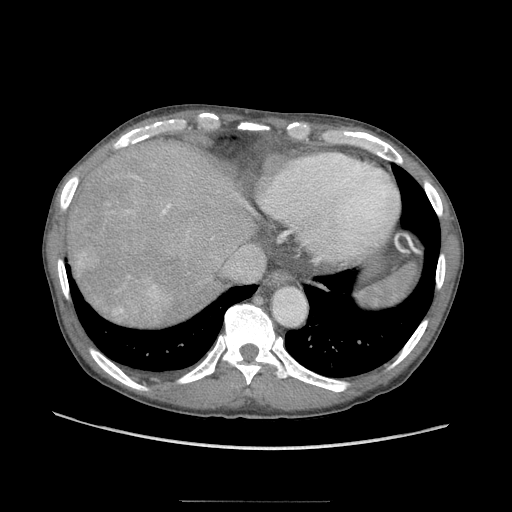
Contrast-enhanced abdominal CT (liver protocol), one axial slice. 120 kVp. Soft-tissue window (W 400 / L 40 HU). 2.5 mm slice thickness. 512 × 512 image matrix, field of view 380 × 380 mm. Case-level facts recorded for this patient, not image findings: diagnosis: hepatocellular carcinoma (patient treated with transarterial chemoembolisation; whether this scan precedes or follows treatment is not stated here); TNM stage (as recorded): Stage-IIIA; Child-Pugh class: A; tumour differentiation: moderately differentiated; tumour nodularity: multinodular.
Annotated regions visible in this slice (semi-automatic segmentation, software-assisted and operator-edited):
- abdominal aorta: box from (x=274, y=289) to (x=305, y=325) px
- liver parenchyma outside the tumour (the mass and vessels are separate outlines, so this box may not span the whole liver): (x=68, y=140)–(x=260, y=316)
- liver vessels: (x=148, y=286)–(x=153, y=289)